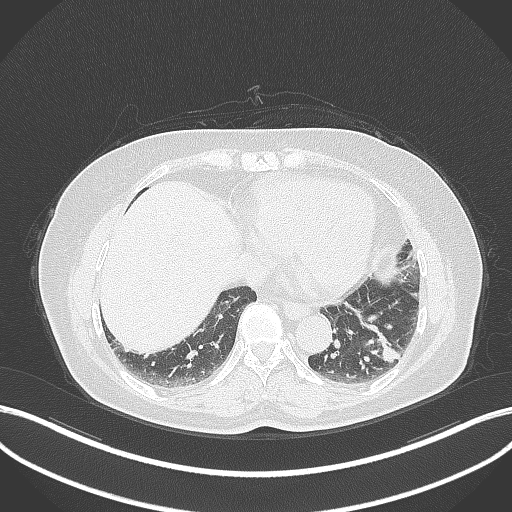
Chest CT, one axial slice. Reconstruction kernel B70f. Lung window (W 1500 / L -600 HU). 512 × 512 image matrix. Patient: female, 59 years. From the clinical record (not read from this slice): clinical TNM (as recorded): T2a N0 M0; histopathological grade: G2-3.
Structures marked on this image (bounding box drawn by a radiologist):
- lung tumour (recorded histology: adenocarcinoma): bounding box (x1, y1, x2, y2) in pixels: (358, 318, 399, 360)